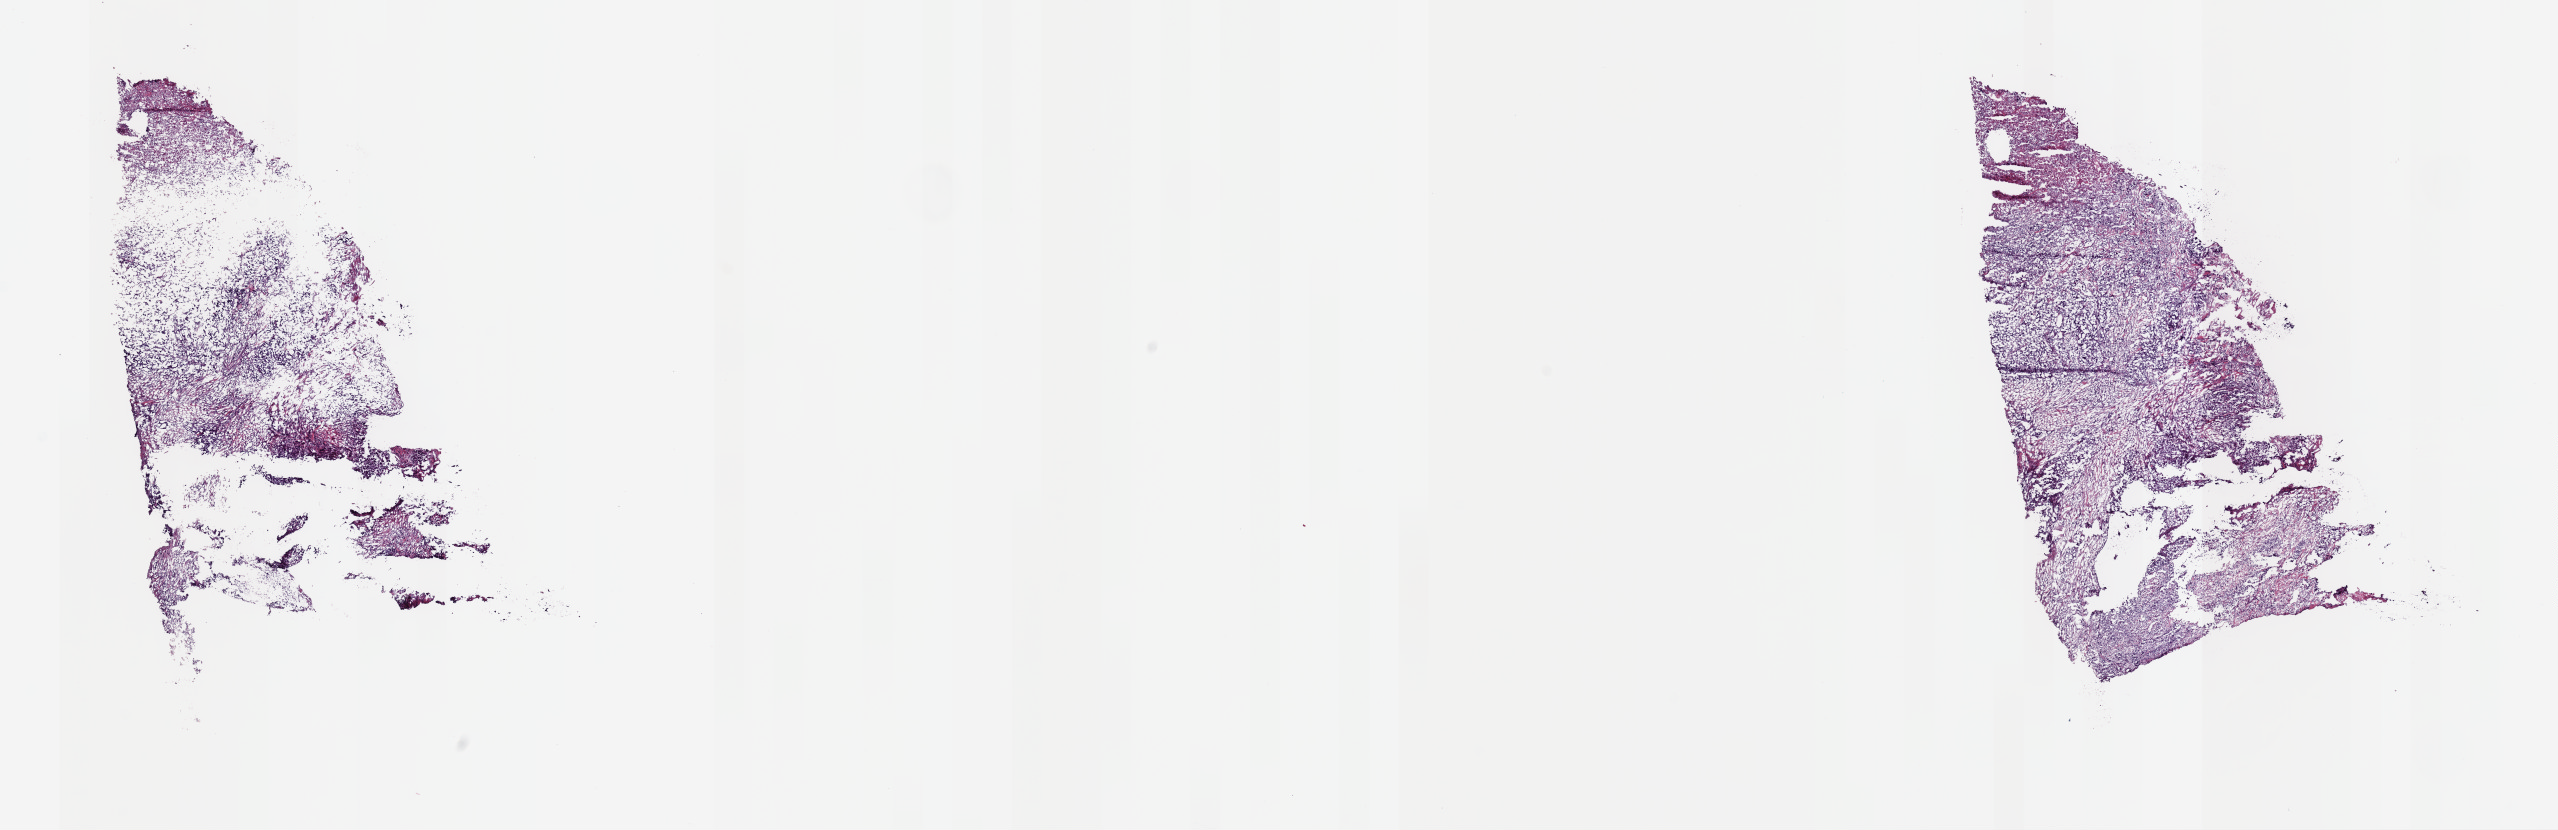
H&E whole-slide image — low-resolution overview of the scanned area, about 20.2 x 6.6 mm (acquisition: 40x scan); frozen section; sample: primary tumour, bladder. Male patient; age at initial diagnosis 66 years.
Pathologic diagnosis: Transitional cell carcinoma (lateral wall of bladder).